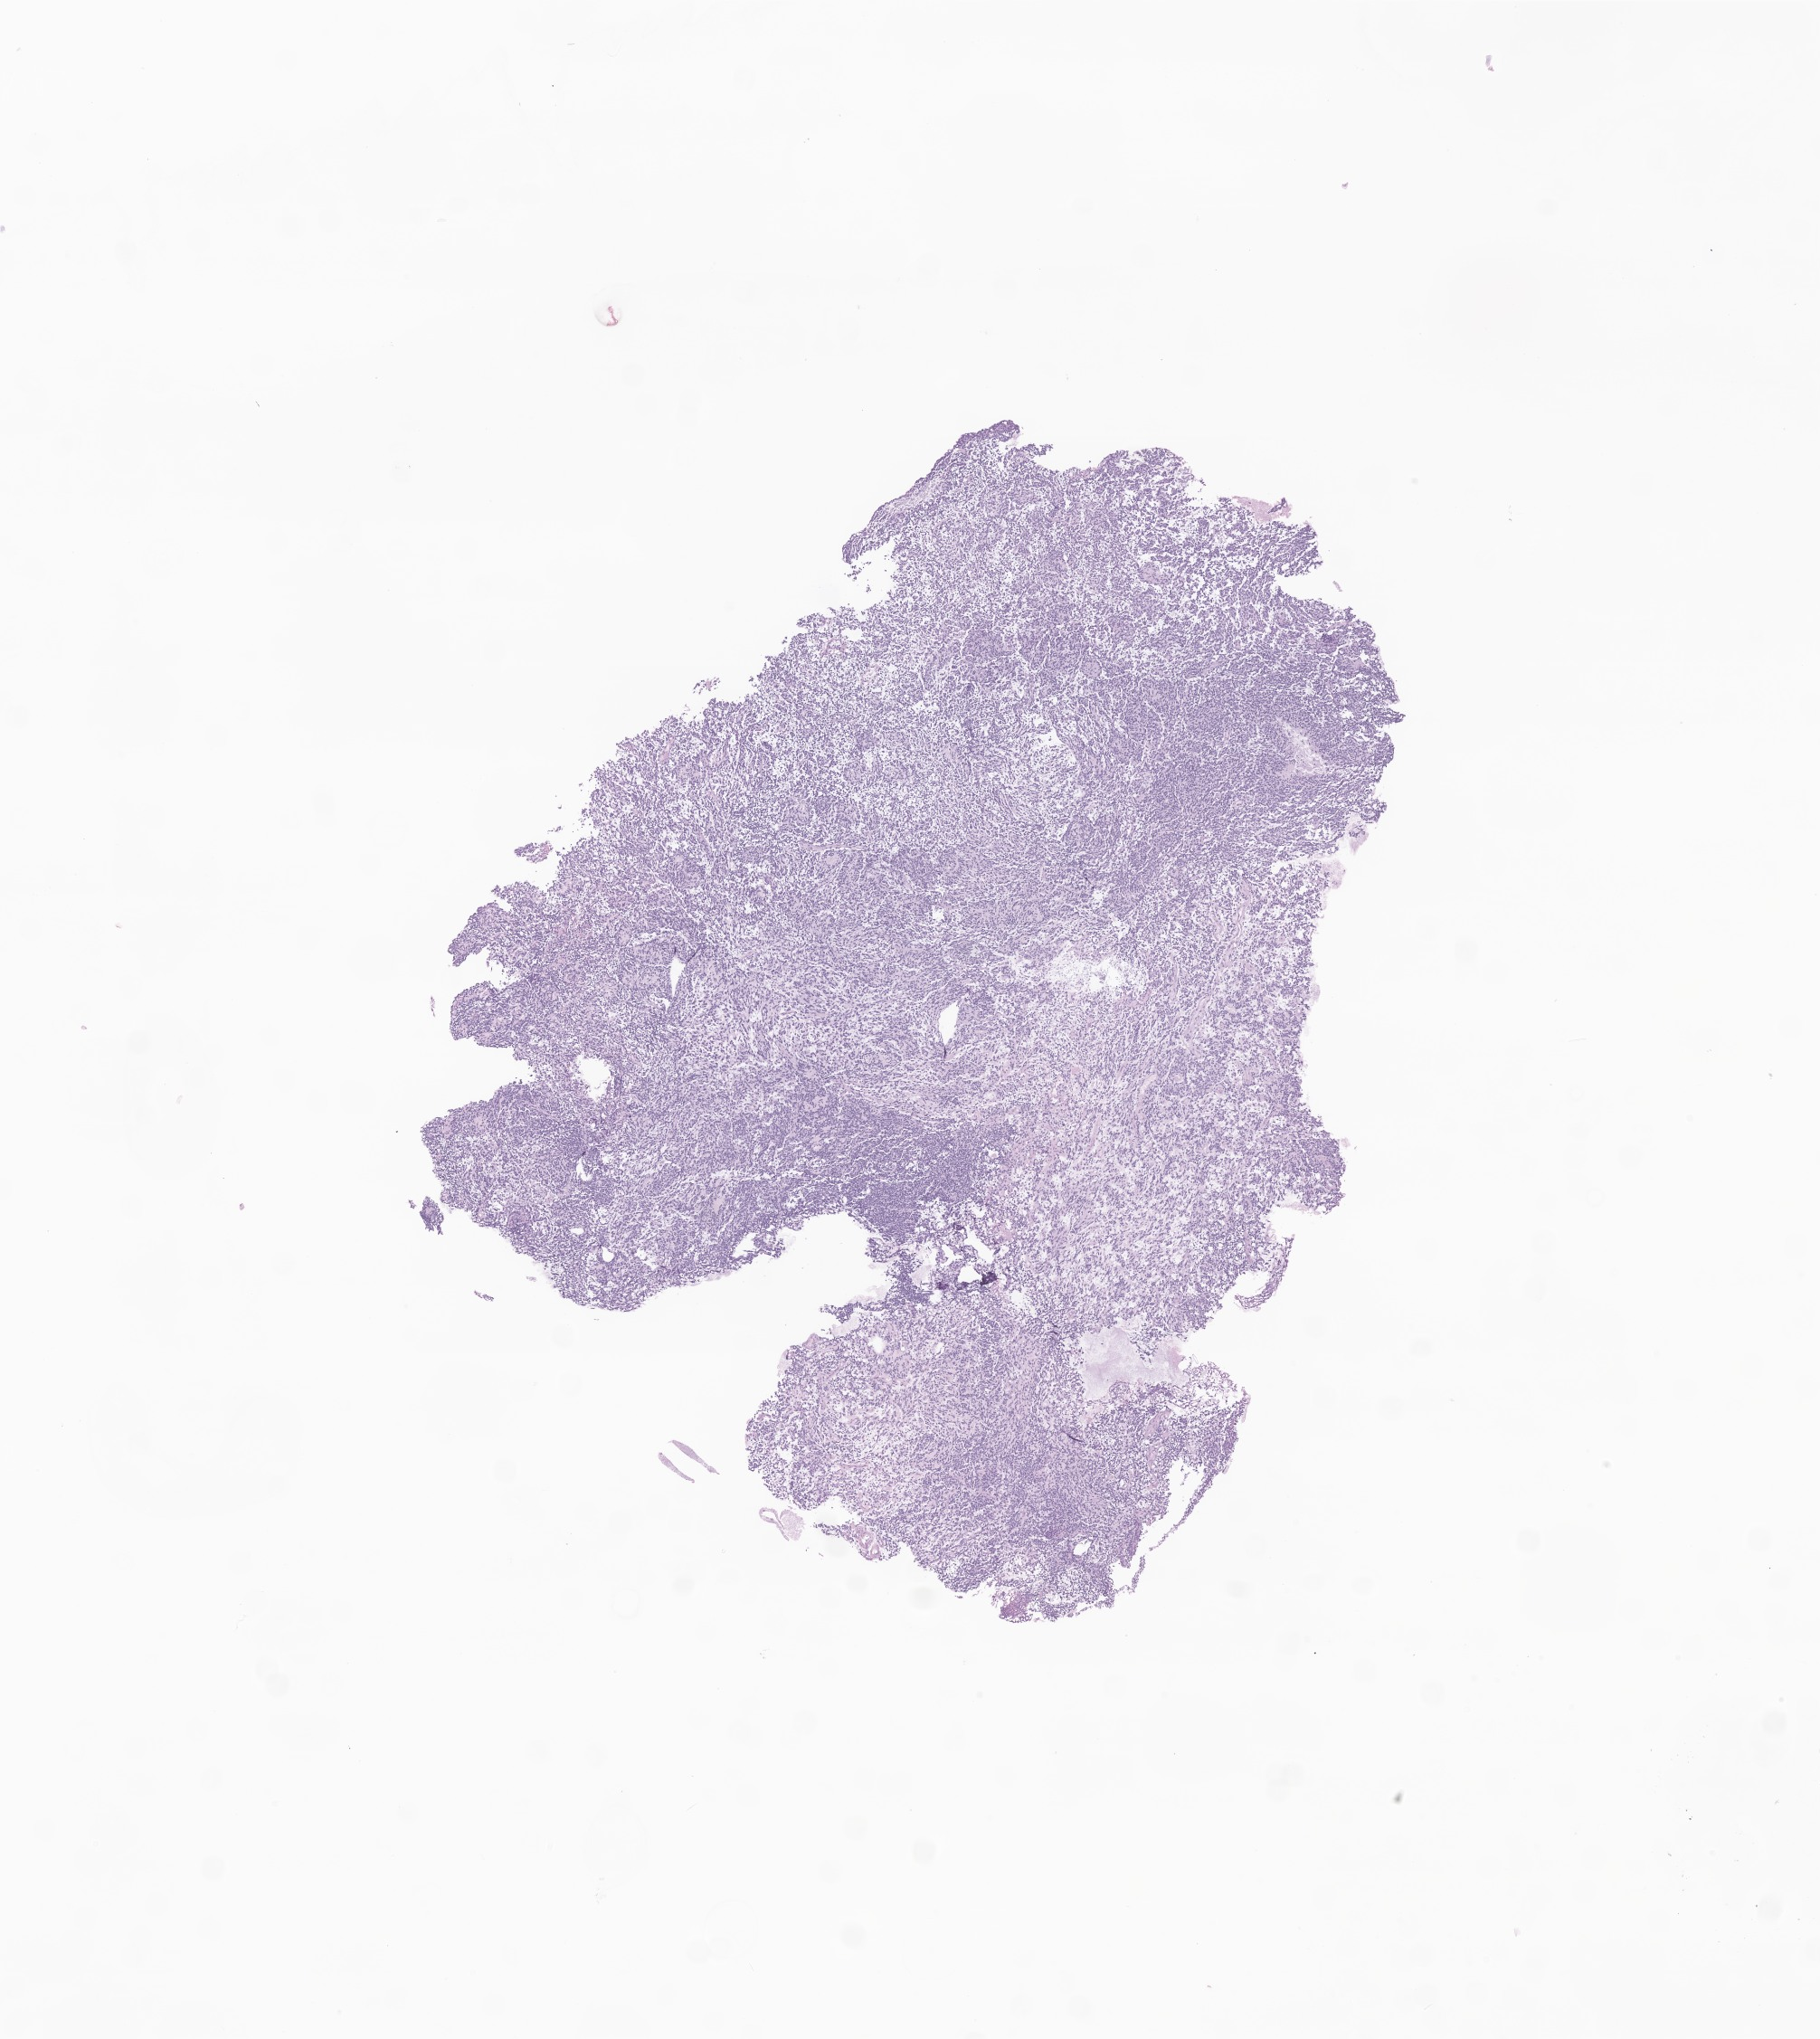
Hematoxylin and eosin (H&E) whole-slide image of tumor tissue from the brain stem, low-resolution overview of the scanned area, about 8.5 x 9.5 mm, formalin-fixed, paraffin-embedded (FFPE) tissue. Female patient, age 37 months.
• recorded diagnosis: Medulloblastoma, NOS